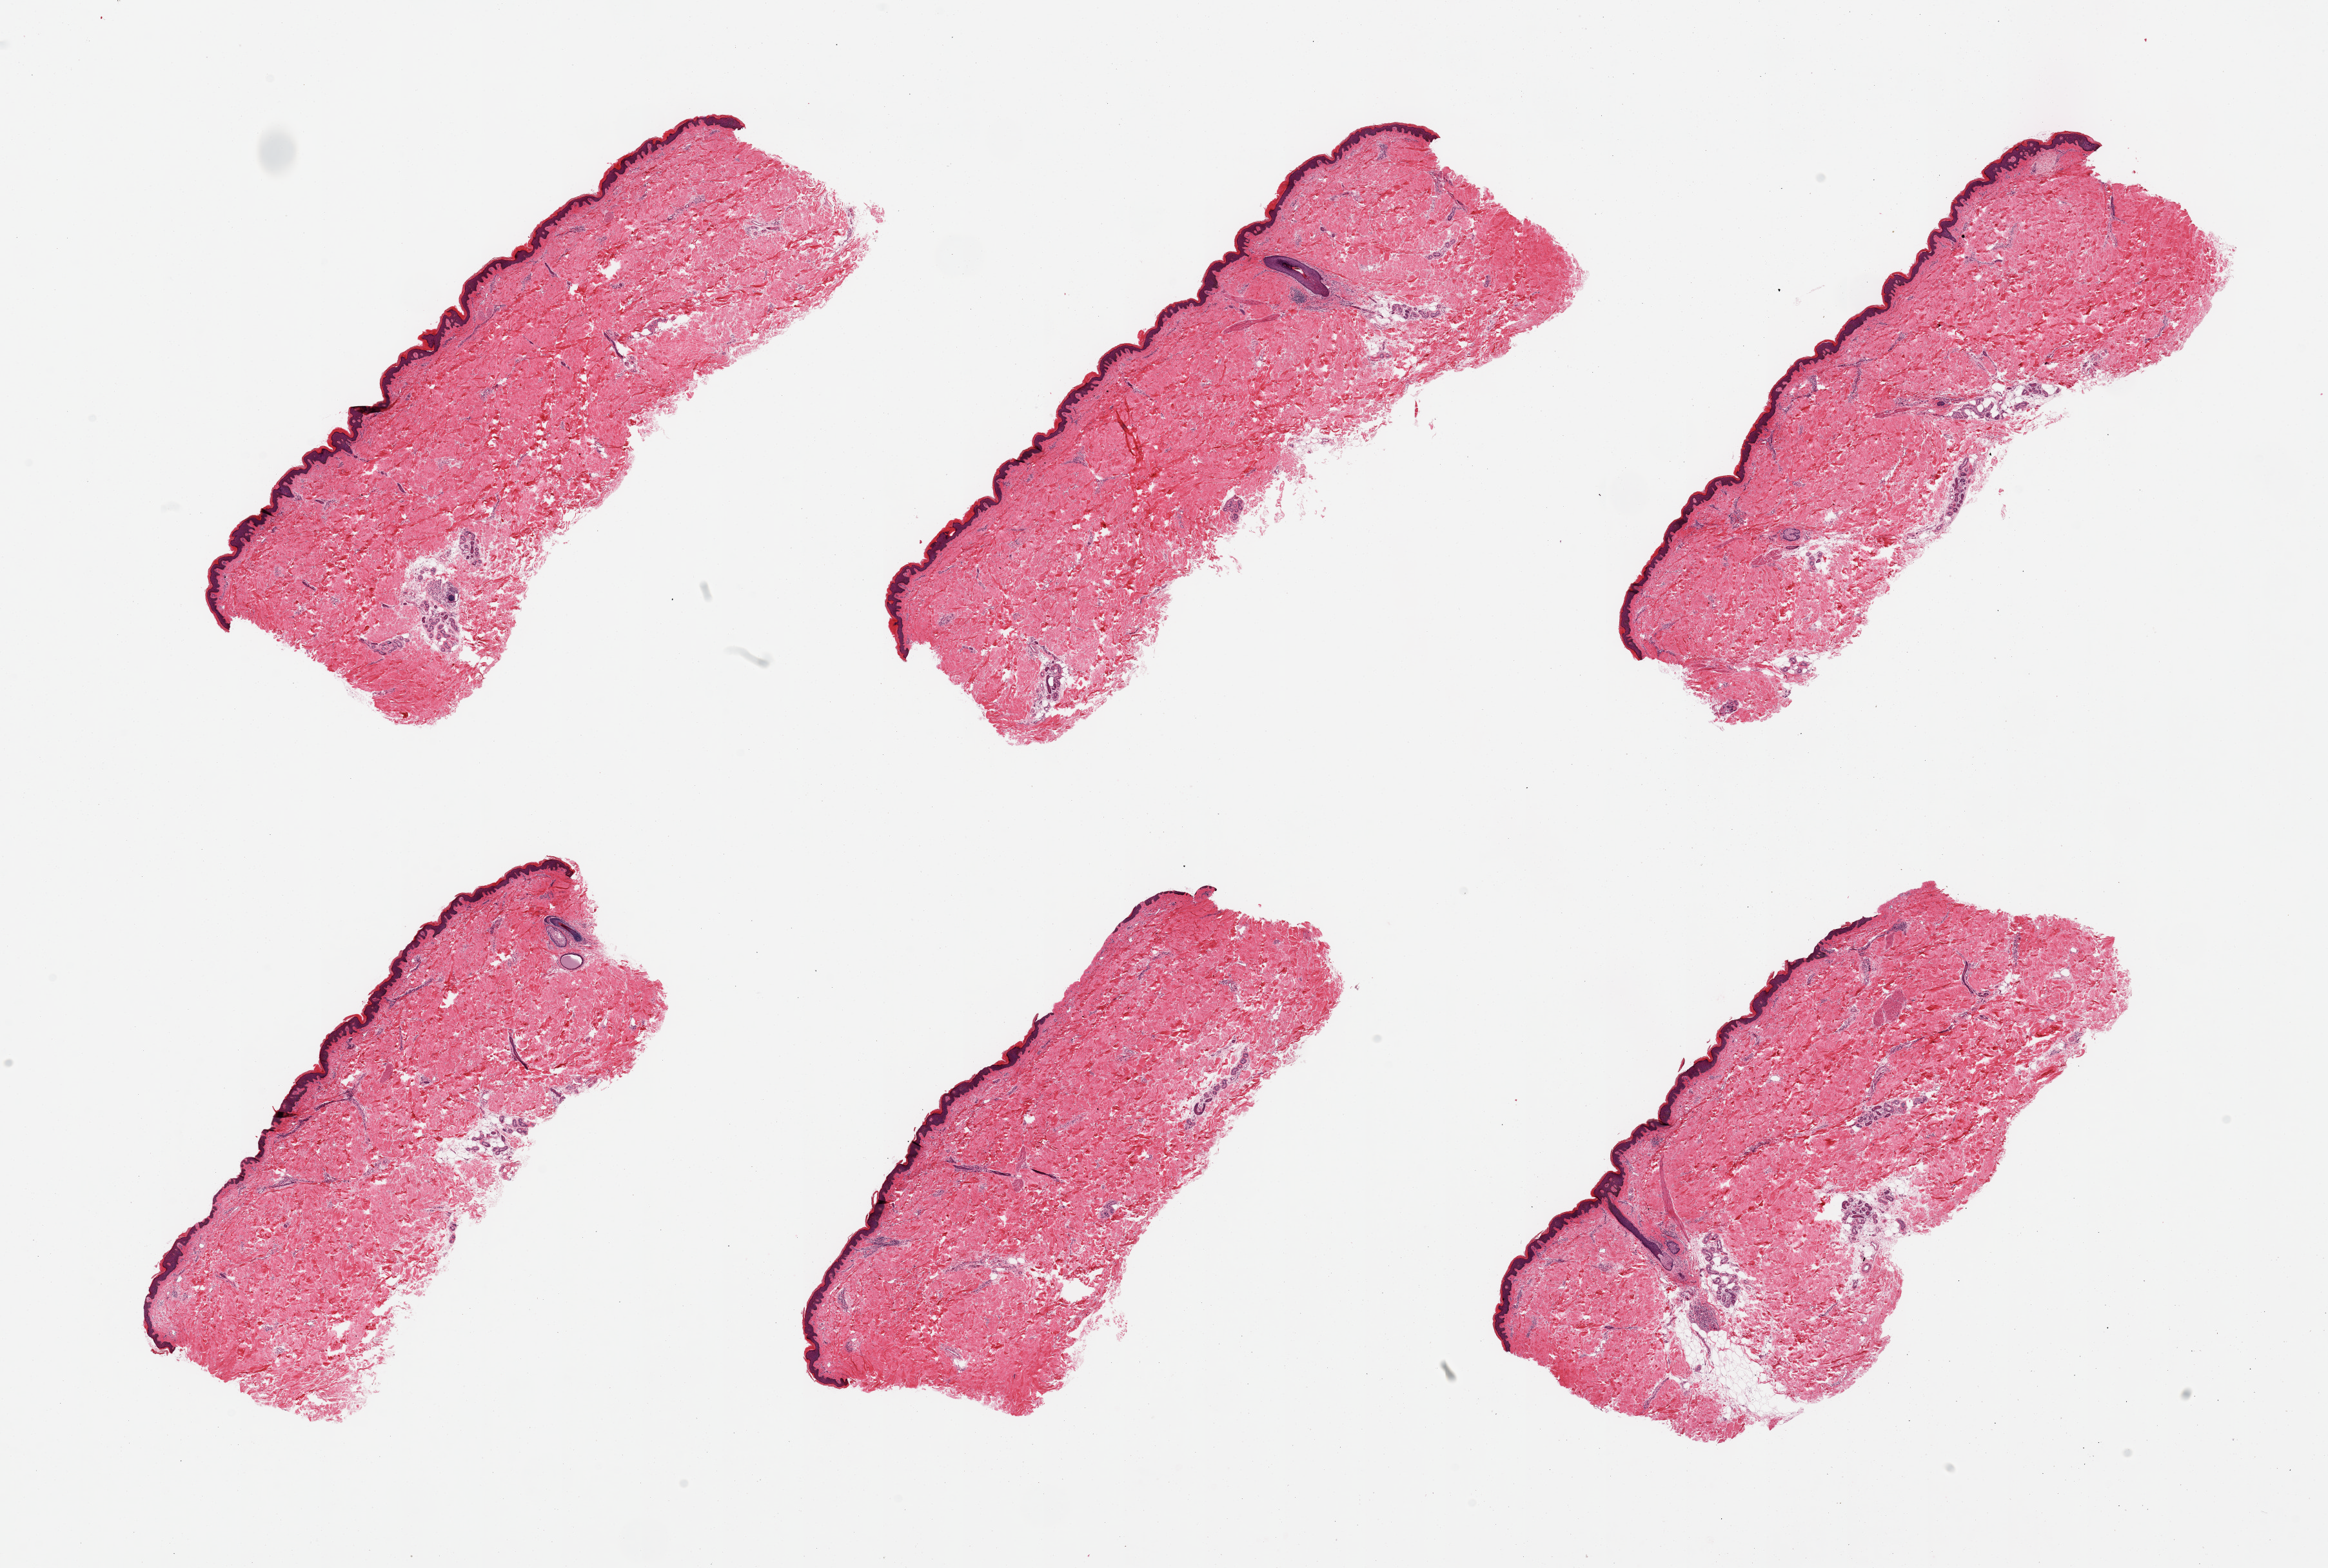
Digitized H&E-stained section, a low-resolution overview of the entire scanned area, about 28.5 x 19.2 mm (from a 20x scan); PAXgene-fixed, paraffin-embedded tissue; target tissue: skin of lower leg; tissue donor sample. Donor sex: male.
Review note (as recorded): 6 pieces; well trimmed; <5% dermal fat.